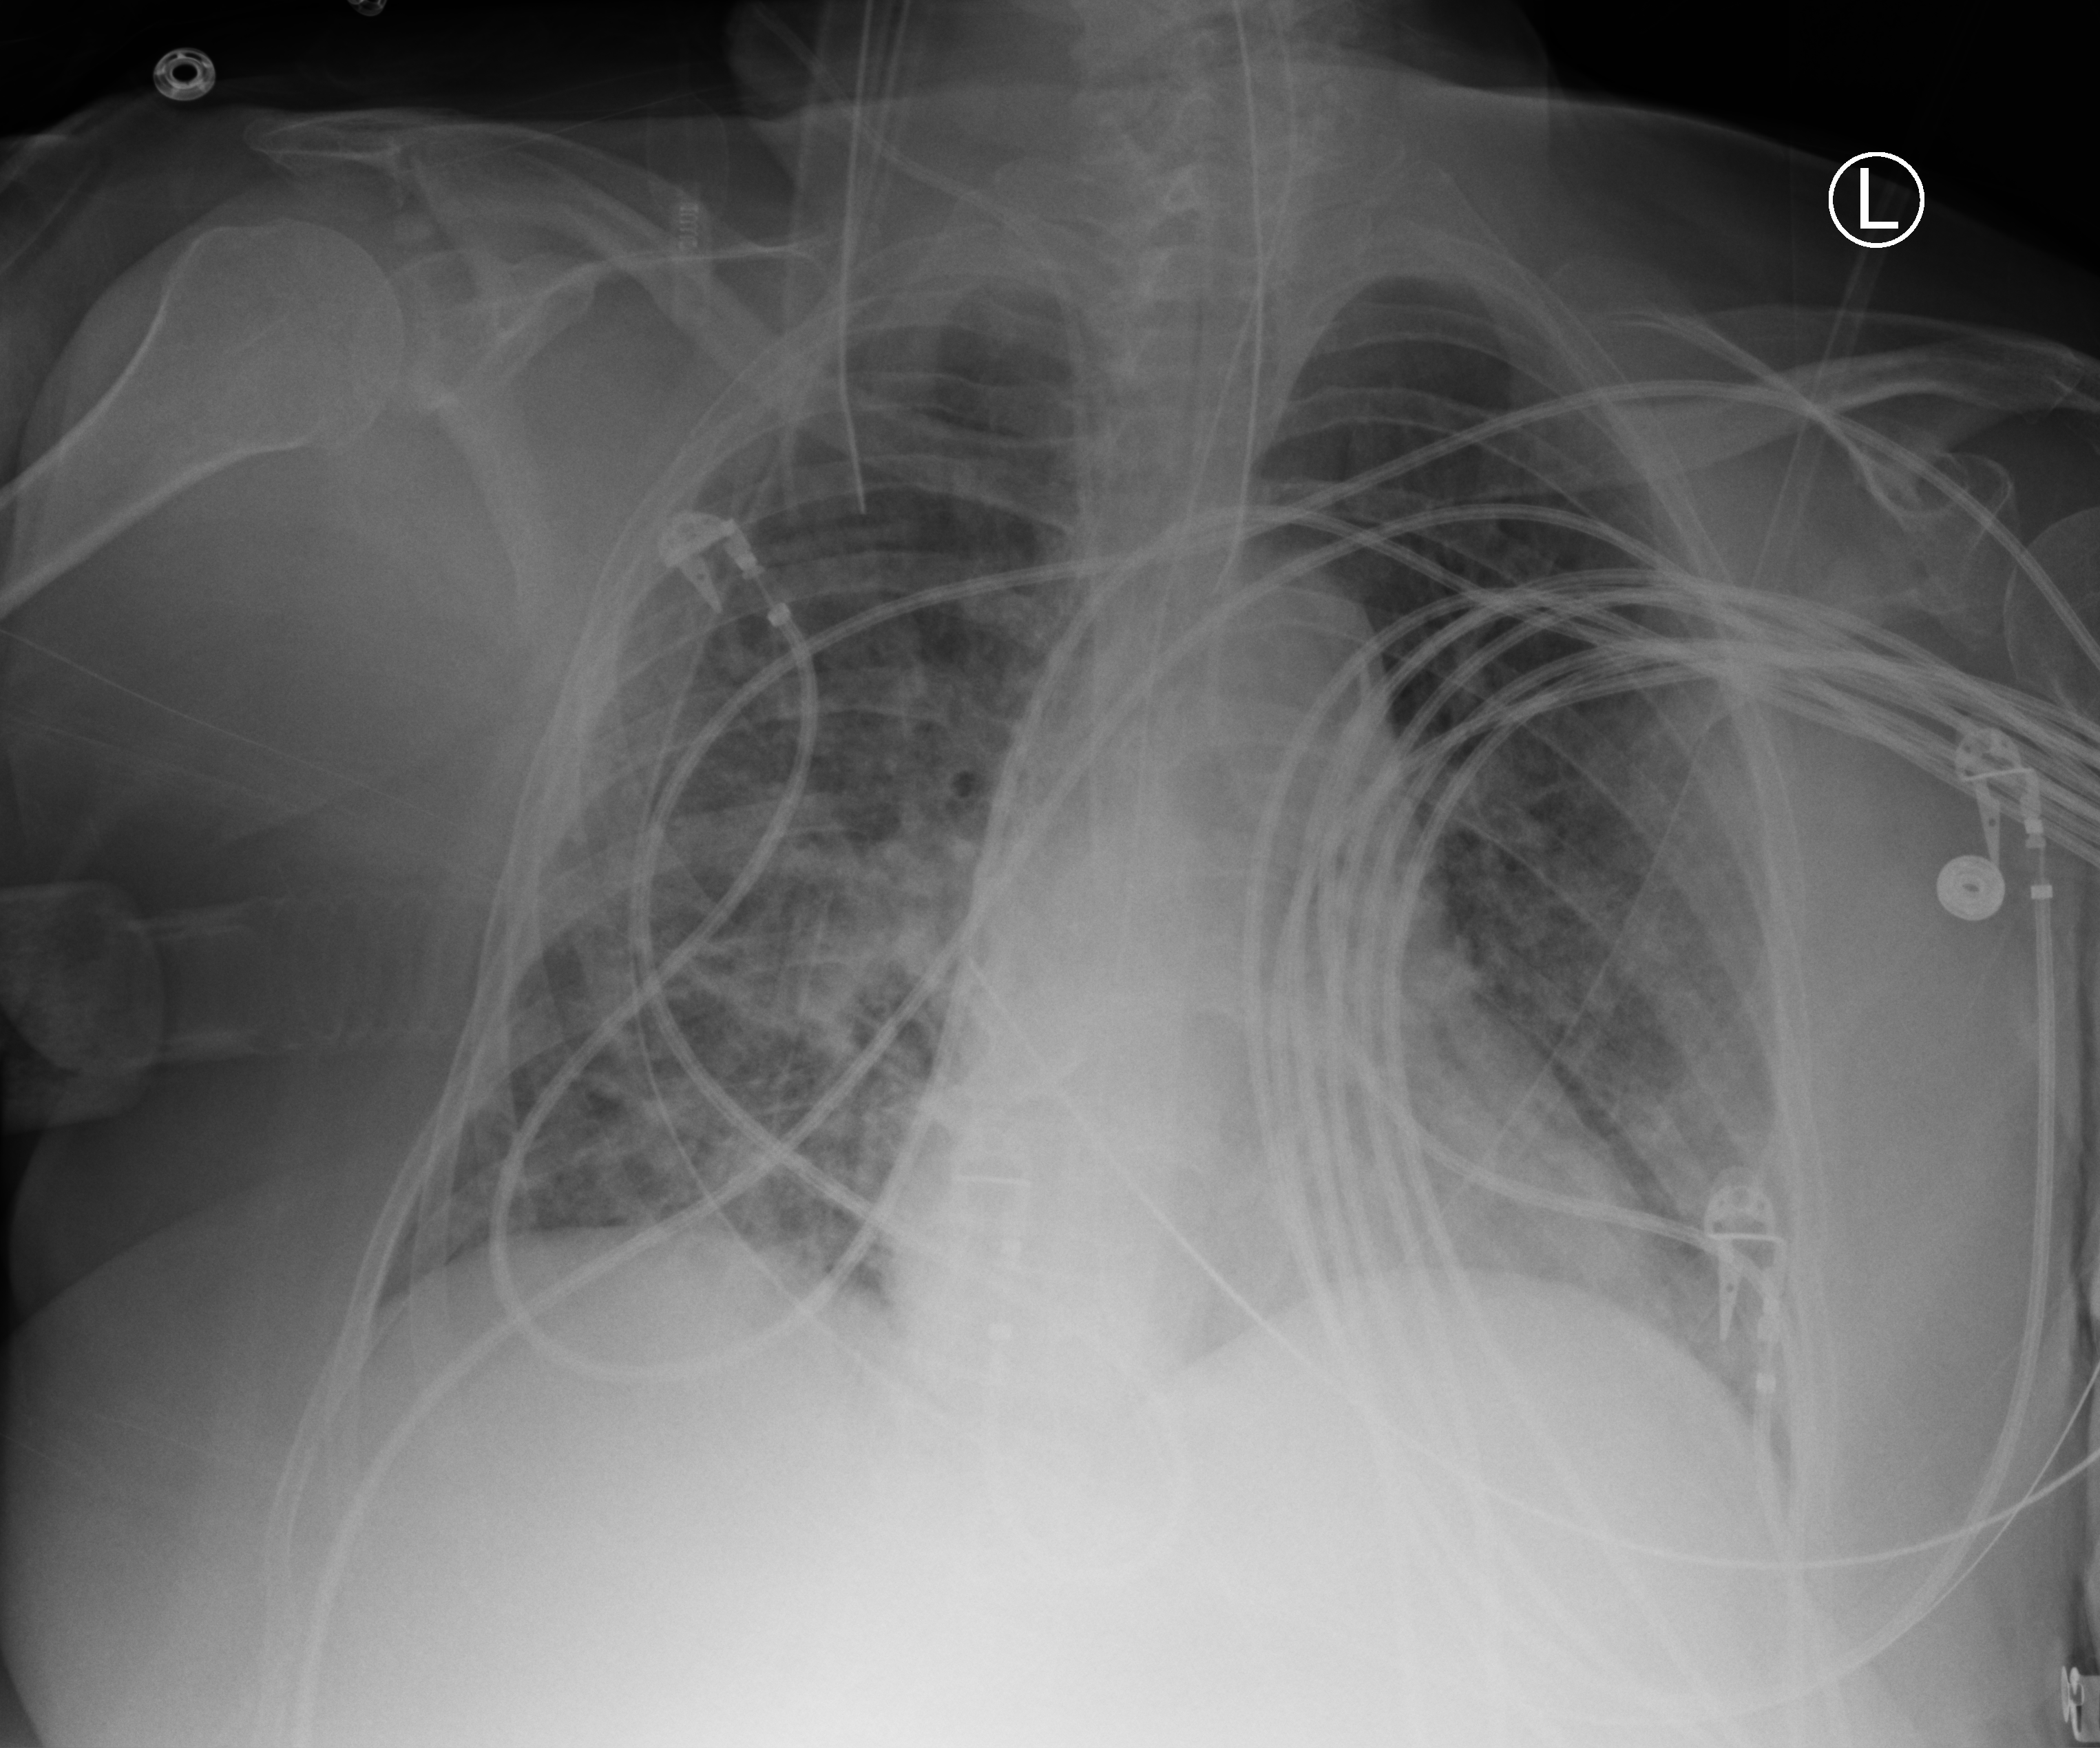
Chest X-ray (portable). Female patient hospitalised with COVID-19, age 75–90 years.
Hospital-stay facts (about this admission, not read from this image; timing relative to this image not recorded): mechanically ventilated during this hospital stay: yes.